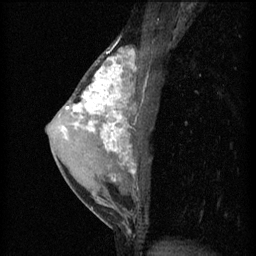
Breast MRI (dynamic contrast-enhanced), one sagittal slice. Position 32 of 60 along the scan axis. 3 images stored at this slice position (order not interpretable as contrast timing). 1.5 T. TE 4.2 ms, TR 11 ms. 2 mm slice thickness. 256 × 256 image matrix, field of view 180 × 180 mm. Female patient, age 40 years.
Outlined on this slice (semi-automatically segmented with operator editing):
- analysis volume of interest (the breast-tissue region the enhancement analysis was run in; not a lesion): bounding box (x1, y1, x2, y2) in pixels: (55, 48, 146, 203)
- tumour enhancement mask (voxels above the 70 % enhancement threshold inside the analysis volume of interest): (66, 50, 137, 175)